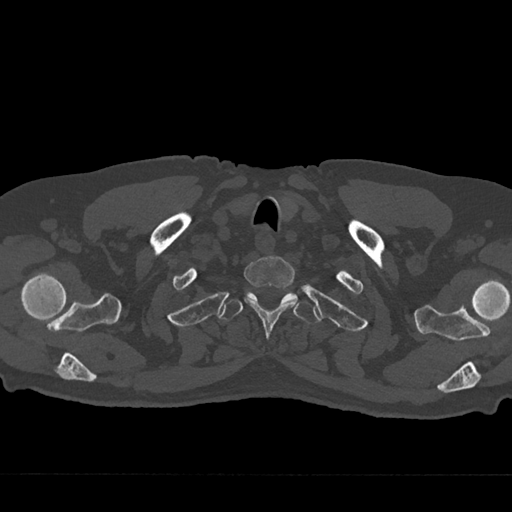
CT including the spine, one axial slice; slice 639 of 797 in the series (ordered by position); reconstruction kernel Br40s/3; 120 kVp; bone window (W 1800 / L 400 HU); 0.5 mm slice thickness; 512 × 512 image matrix. Patient: male, 75 years. Case-level facts recorded for this patient, not image findings: primary cancer: renal.
Structures marked on this image (semi-automatically segmented with operator editing):
- T1 vertebra: bounding box (x1, y1, x2, y2) in pixels: (244, 256, 298, 338)
- T2 vertebra: (218, 292, 320, 324)